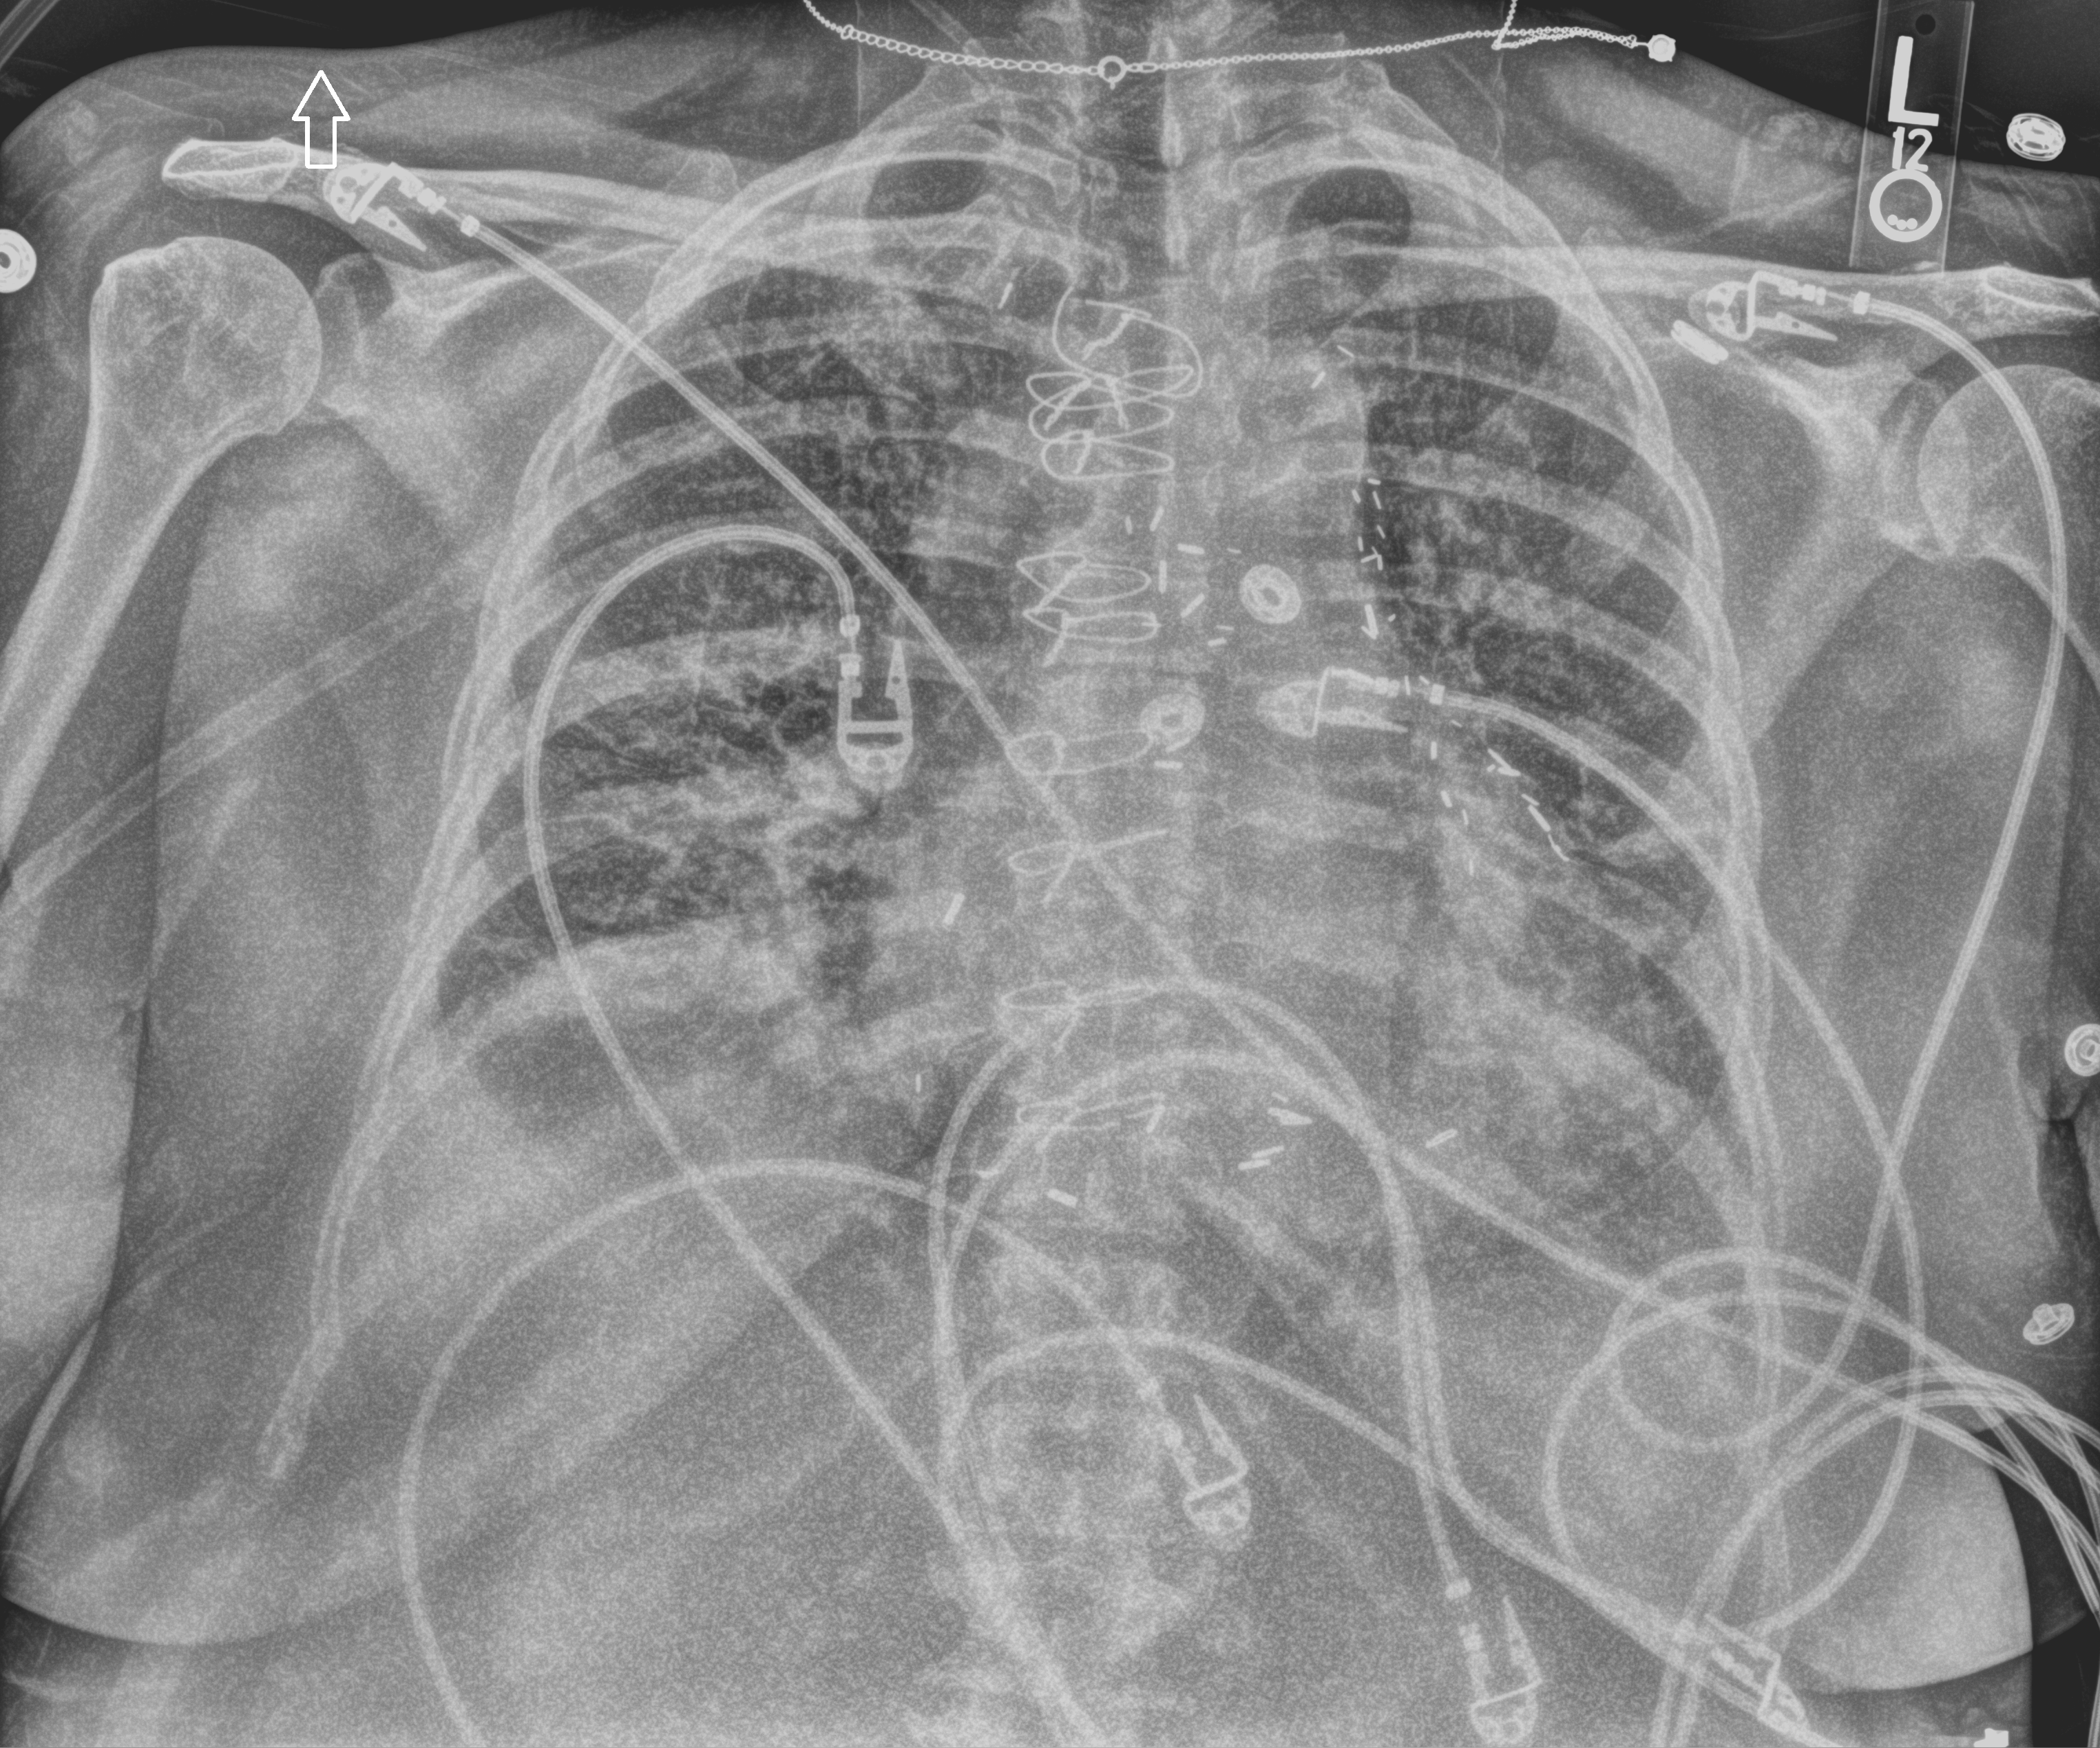
Bedside chest radiograph (computed radiography); anteroposterior (AP) projection. Patient hospitalised with COVID-19; female, aged 60–74 years.
Admission-level facts for this patient (not findings on this image; timing relative to this image not recorded): mechanically ventilated during this hospital stay: yes; length of hospital stay: 25 days.